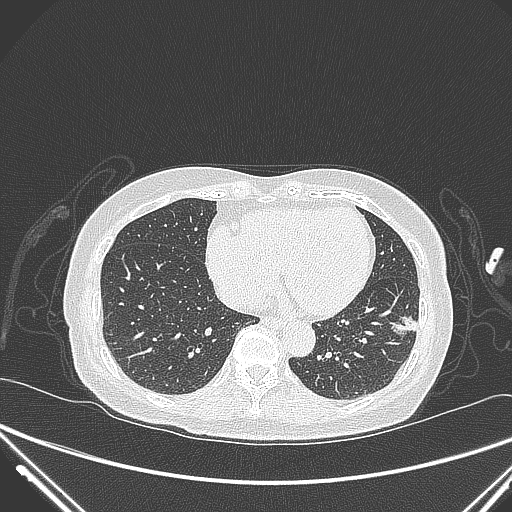
Chest CT, one axial slice; position 104 of 310 along the scan axis; lung window (W 1500 / L -600 HU); 512 × 512 image matrix, field of view 377 × 377 mm. Female patient, age 82 years. Case-level facts recorded for this patient, not image findings: clinical TNM (as recorded): T1c N0 M0; histopathological grade: G2.
Structures marked on this image (bounding box drawn by a radiologist):
- lung tumour (recorded histology: adenocarcinoma): box from (x=387, y=307) to (x=428, y=349) px